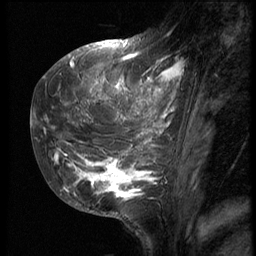
Breast MRI (dynamic contrast-enhanced), one sagittal slice. Slice 19 of 62 in the series (ordered by position). 3 images stored at this slice position (order not interpretable as contrast timing). 1.5 T. TE 4.2 ms, TR 9 ms. 2.5 mm slice thickness. 256 × 256 image matrix, field of view 180 × 180 mm. Patient: female, 28 years. From the clinical record (not read from this slice): setting: breast cancer imaged before/during neoadjuvant chemotherapy.
Annotated regions visible in this slice (semi-automatic segmentation, software-assisted and operator-edited):
- analysis volume of interest (the breast-tissue region the enhancement analysis was run in; not a lesion): bounding box (x1, y1, x2, y2) in pixels: (42, 48, 191, 207)
- tumour enhancement mask (voxels above the 140 % enhancement threshold inside the analysis volume of interest): (42, 50, 184, 199)